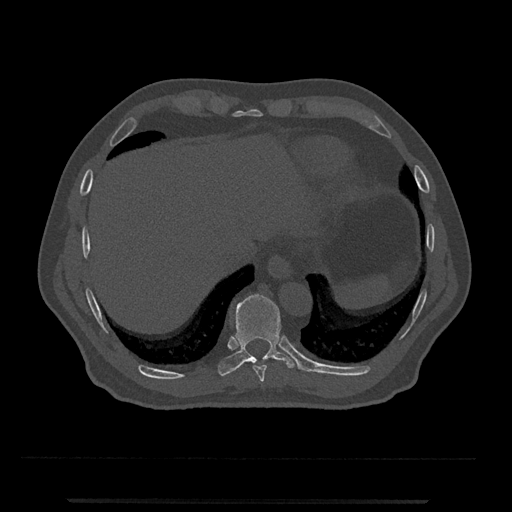
CT including the spine, one axial slice; reconstruction kernel Br40s/3; 120 kVp; bone window (W 1800 / L 400 HU); 0.5 mm slice thickness; 512 × 512 image matrix, field of view 419 × 419 mm. Patient: male, 63 years. From the clinical record (not read from this slice): primary cancer: prostate.
Outlined on this slice (semi-automatic segmentation, software-assisted and operator-edited):
- T10 vertebra: box from (x=218, y=294) to (x=299, y=376) px
- T9 vertebra: (x=253, y=364)–(x=267, y=382)